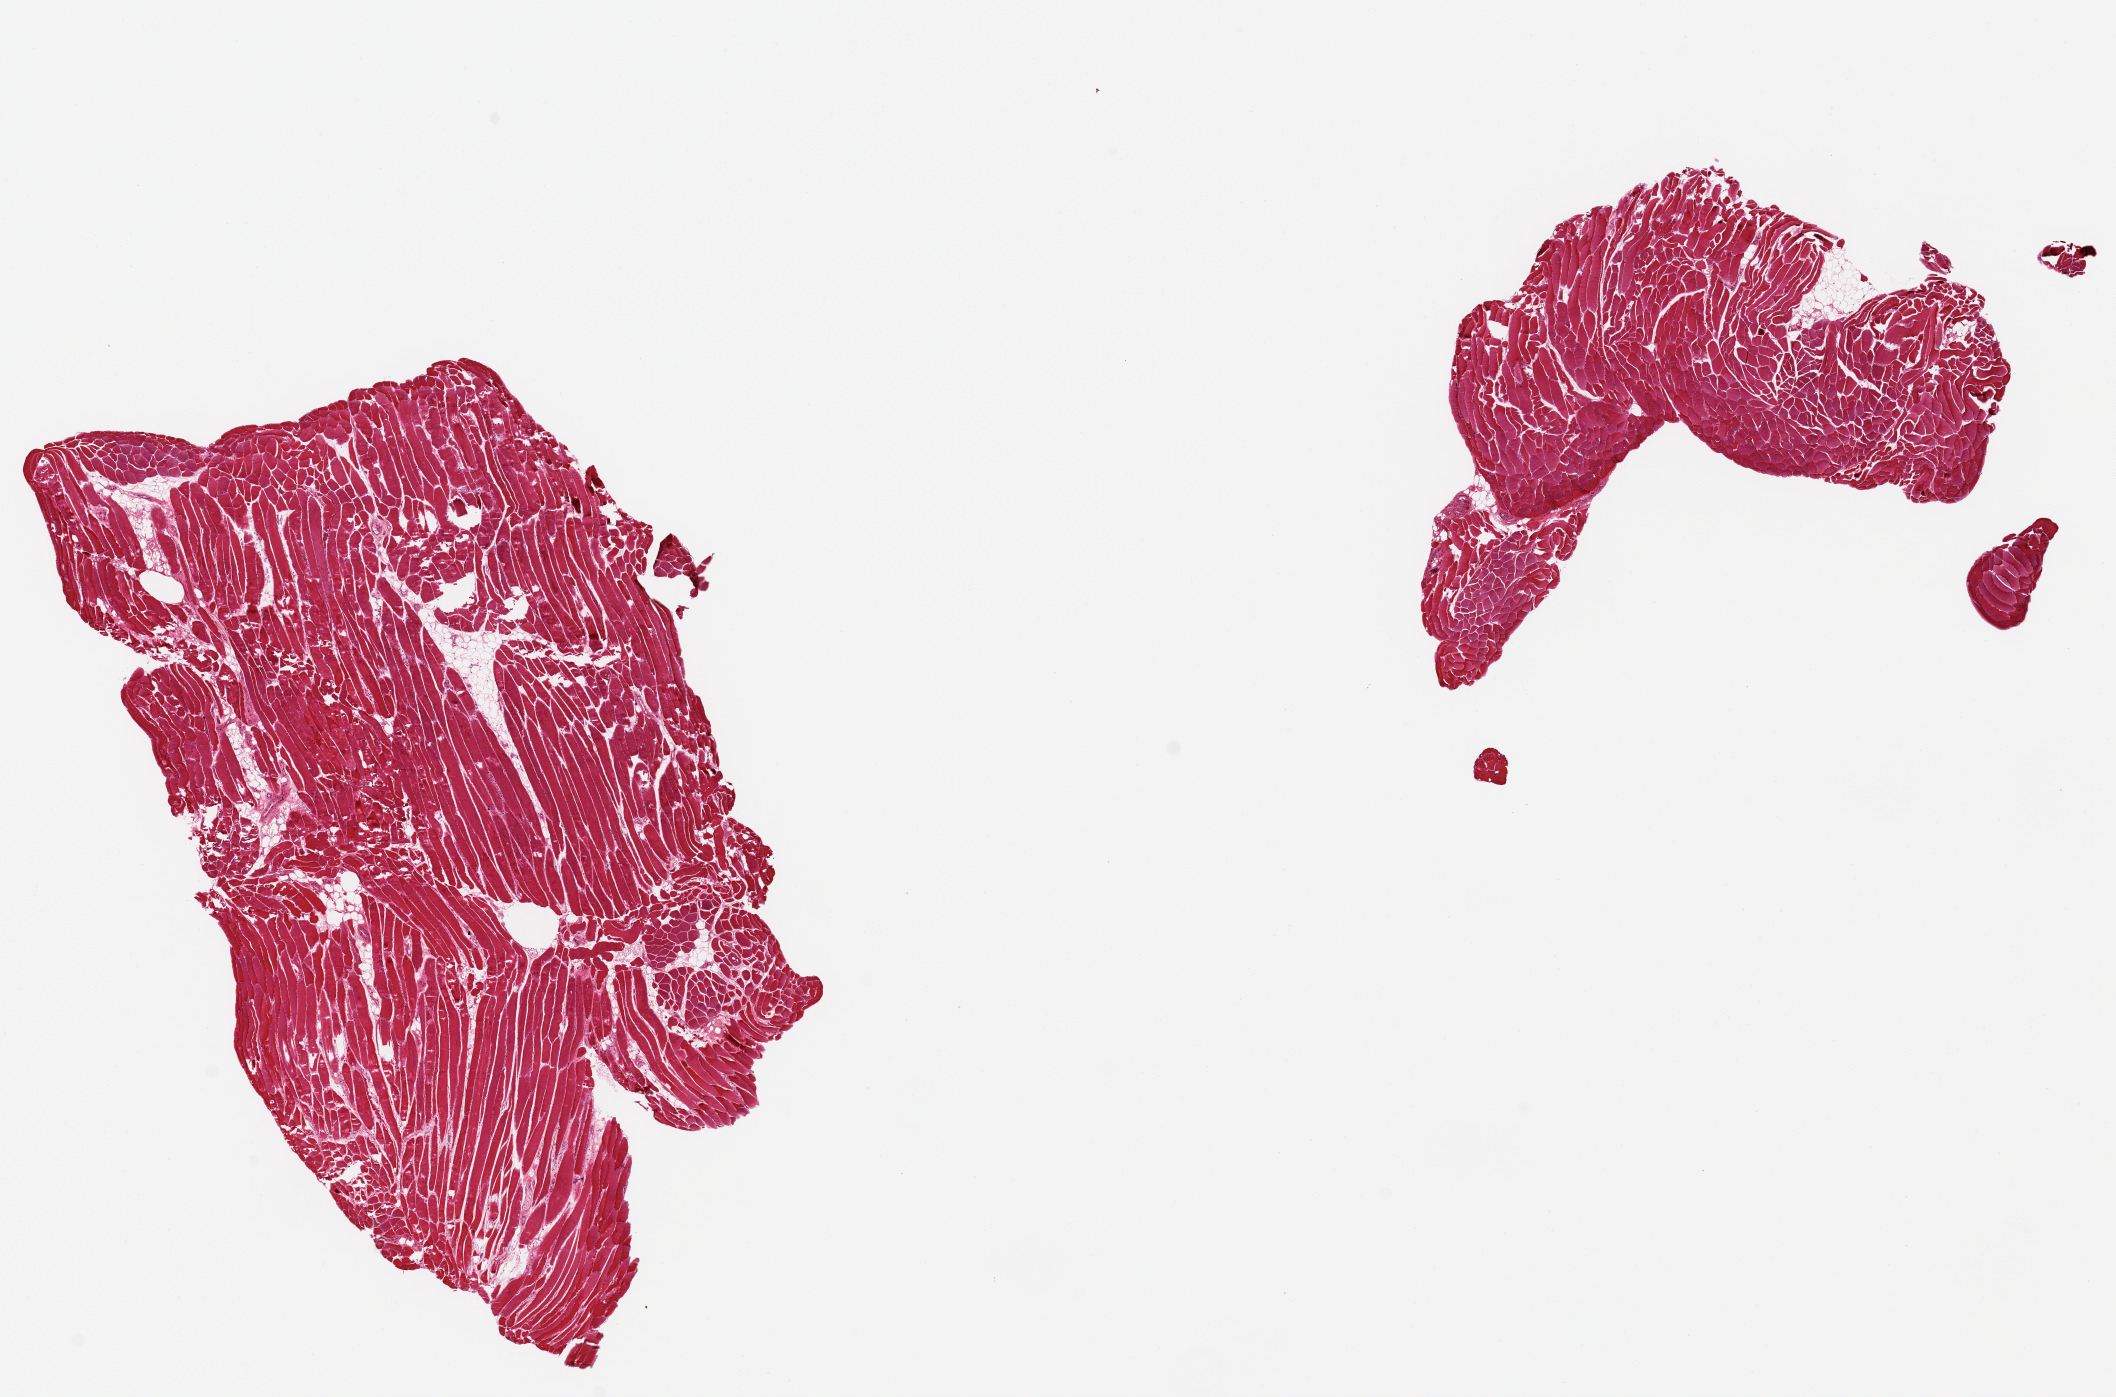
Whole-slide image, hematoxylin and eosin (H&E) stain, brightfield — a low-resolution overview of the entire scanned area, about 16.7 x 11.0 mm, PAXgene-fixed, paraffin-embedded tissue, section of skeletal muscle (target tissue), donor tissue sample. Male donor.
Pathologist's review note for this sample: 2 pieces, 8x5 & 5x3mm; no significant adipose tissue.